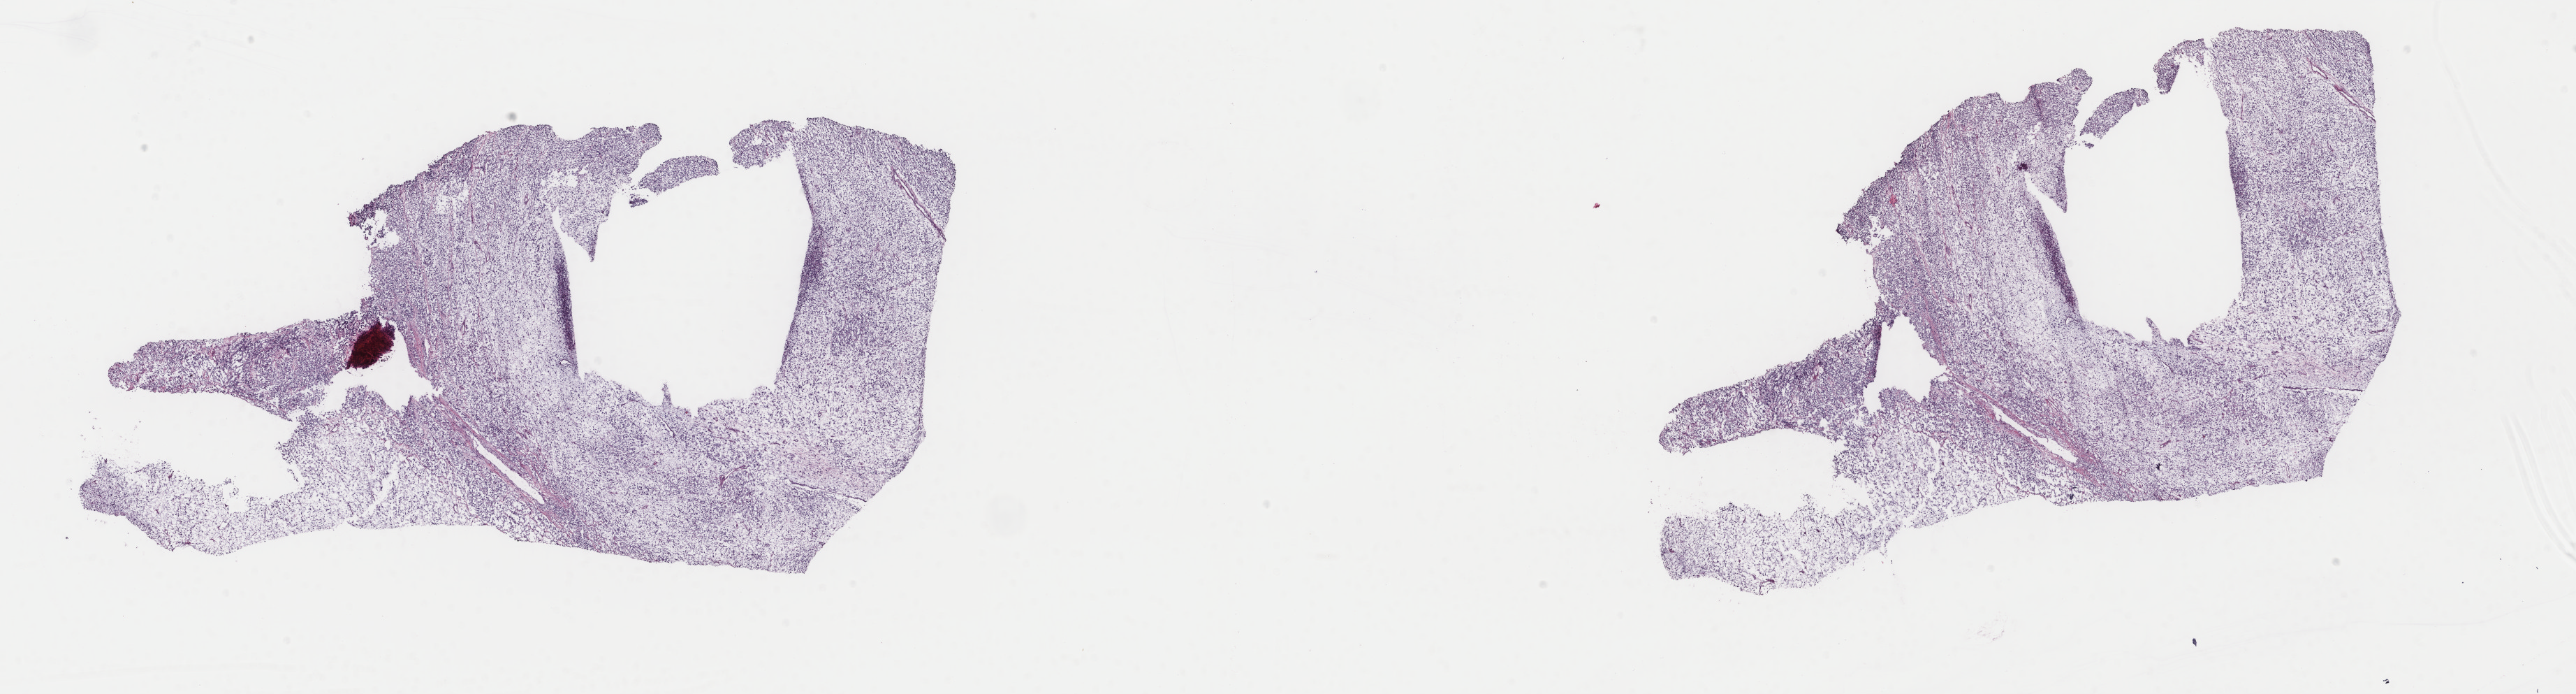
Whole-slide histology image, H&E — whole scanned area (about 29.3 x 7.9 mm, from a 40x scan) shown as a low-resolution overview. Frozen section. Sample: primary tumour, uterus. Female, age 60 years at initial diagnosis. Pathologist review of this section (percent, as recorded): tumour cells 100%, tumour nuclei 80%, normal cells 0%, stromal cells 0%, necrosis 0%. Inflammatory infiltration, as recorded: lymphocyte infiltration 2%, monocyte infiltration 0%, neutrophil infiltration 0%.
* diagnosis: Carcinosarcoma, NOS
* FIGO stage: IVB